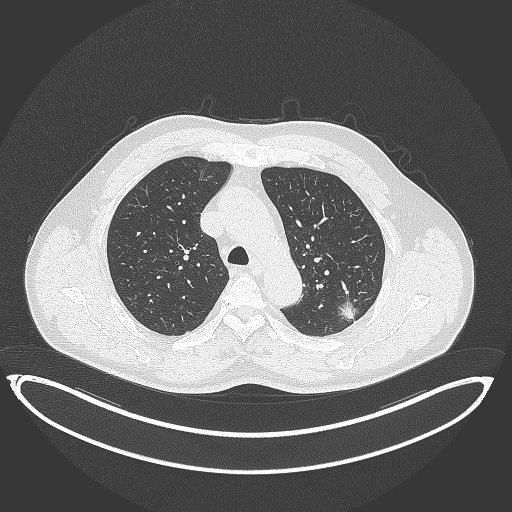
Chest CT, one axial slice. Position 263 of 399 along the scan axis. Reconstruction kernel B70f. Lung window (W 1500 / L -600 HU). 1 mm slice thickness. 512 × 512 image matrix, field of view 469 × 469 mm. Patient: male, 58 years. Case-level facts recorded for this patient, not image findings: clinical TNM (as recorded): T1c N0 M0; histopathological grade: G1-2.
Structures marked on this image (bounding box drawn by a radiologist):
- lung tumour (recorded histology: adenocarcinoma): box from (x=335, y=296) to (x=362, y=323) px